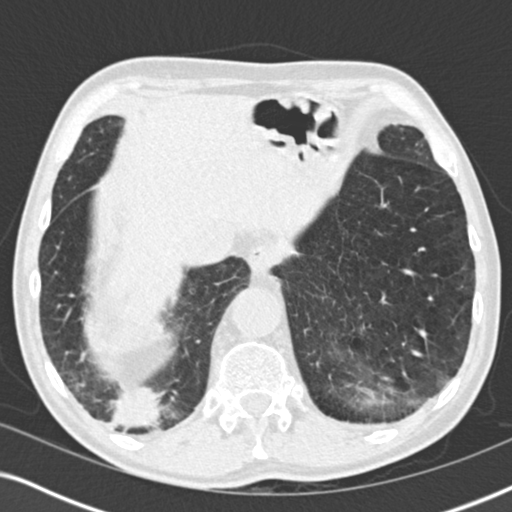
Low-dose screening chest CT, one axial slice; slice 51 of 196 in the series (ordered by position); reconstruction kernel B30f; 120 kVp; lung window (W 1500 / L -600 HU); 2 mm slice thickness; 512 × 512 image matrix, field of view 330 × 330 mm.
Outlined on this slice (manually delineated by an expert):
- lesion 3 (tumor, lower lobe of right lung): box from (x=110, y=385) to (x=166, y=429) px